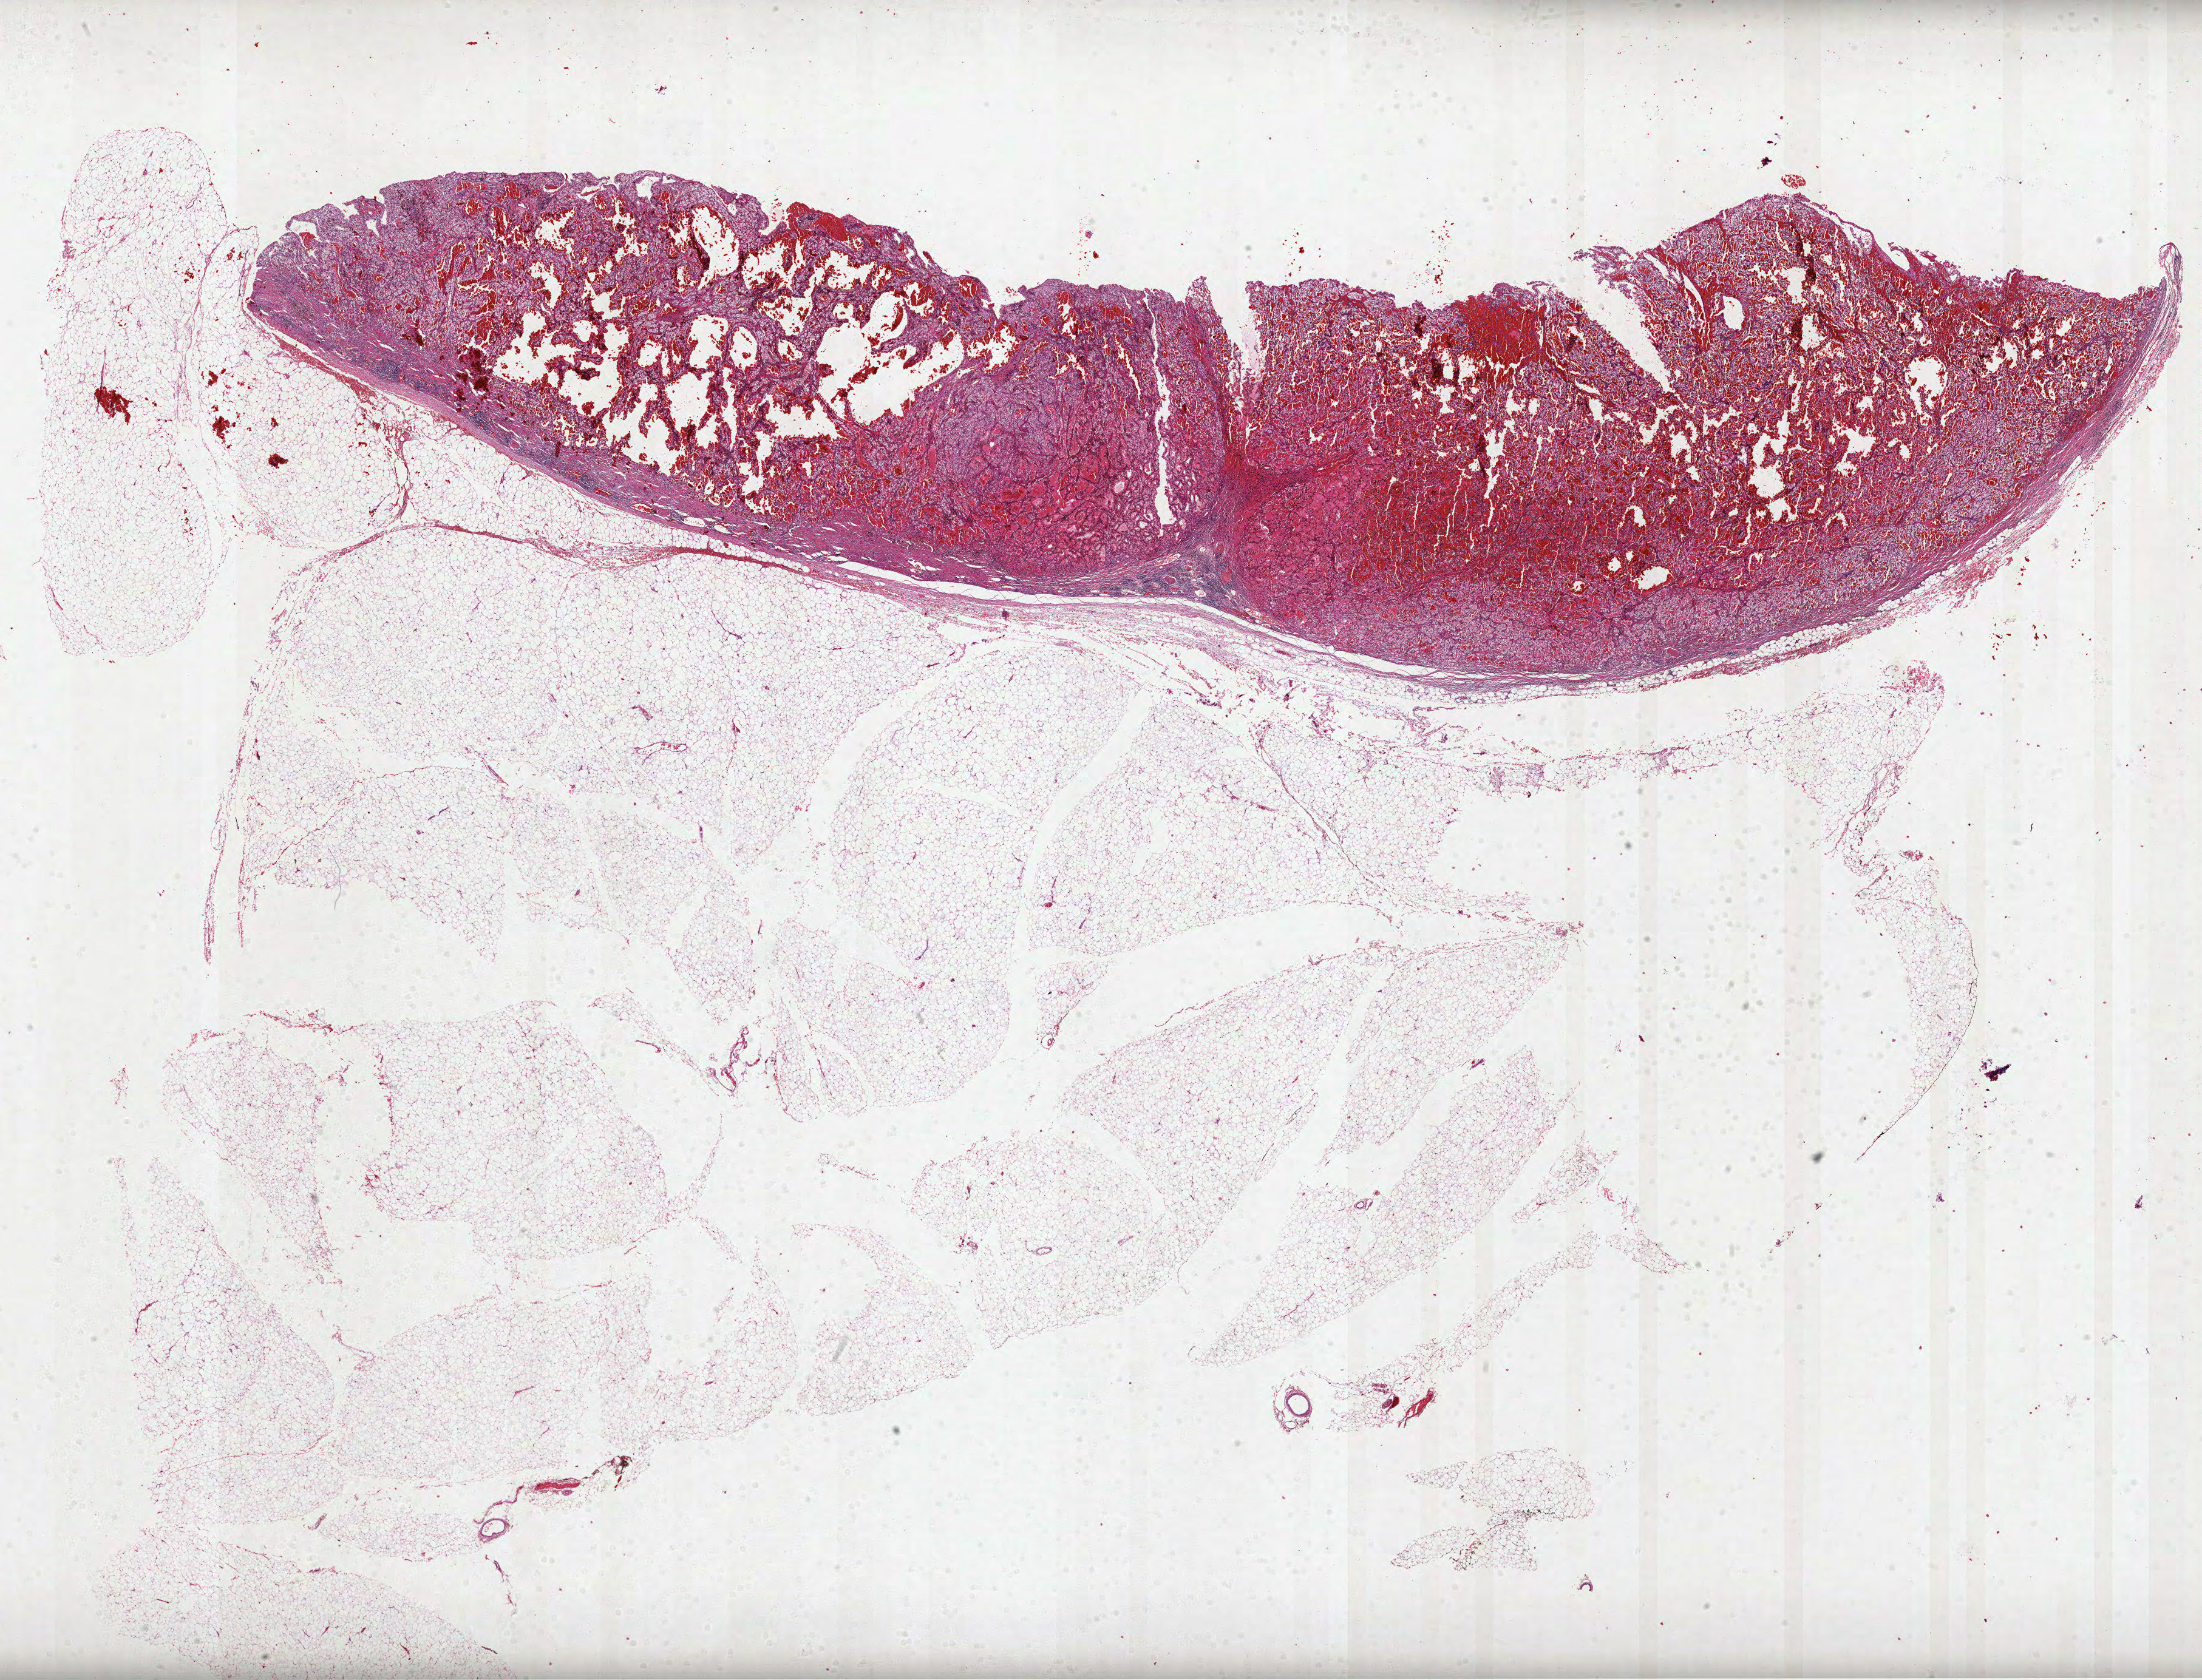
Whole-slide histology image, H&E-stained, low-resolution overview of the scanned area, about 29.2 x 22.3 mm, formalin-fixed paraffin-embedded (FFPE) diagnostic section, primary tumour sample from the kidney. Male, age 77 years at initial diagnosis. Histologic grade: G3 (poorly differentiated).
TNM: T1a N0 M0. Diagnosis: Clear cell adenocarcinoma, NOS. AJCC pathologic stage: I.